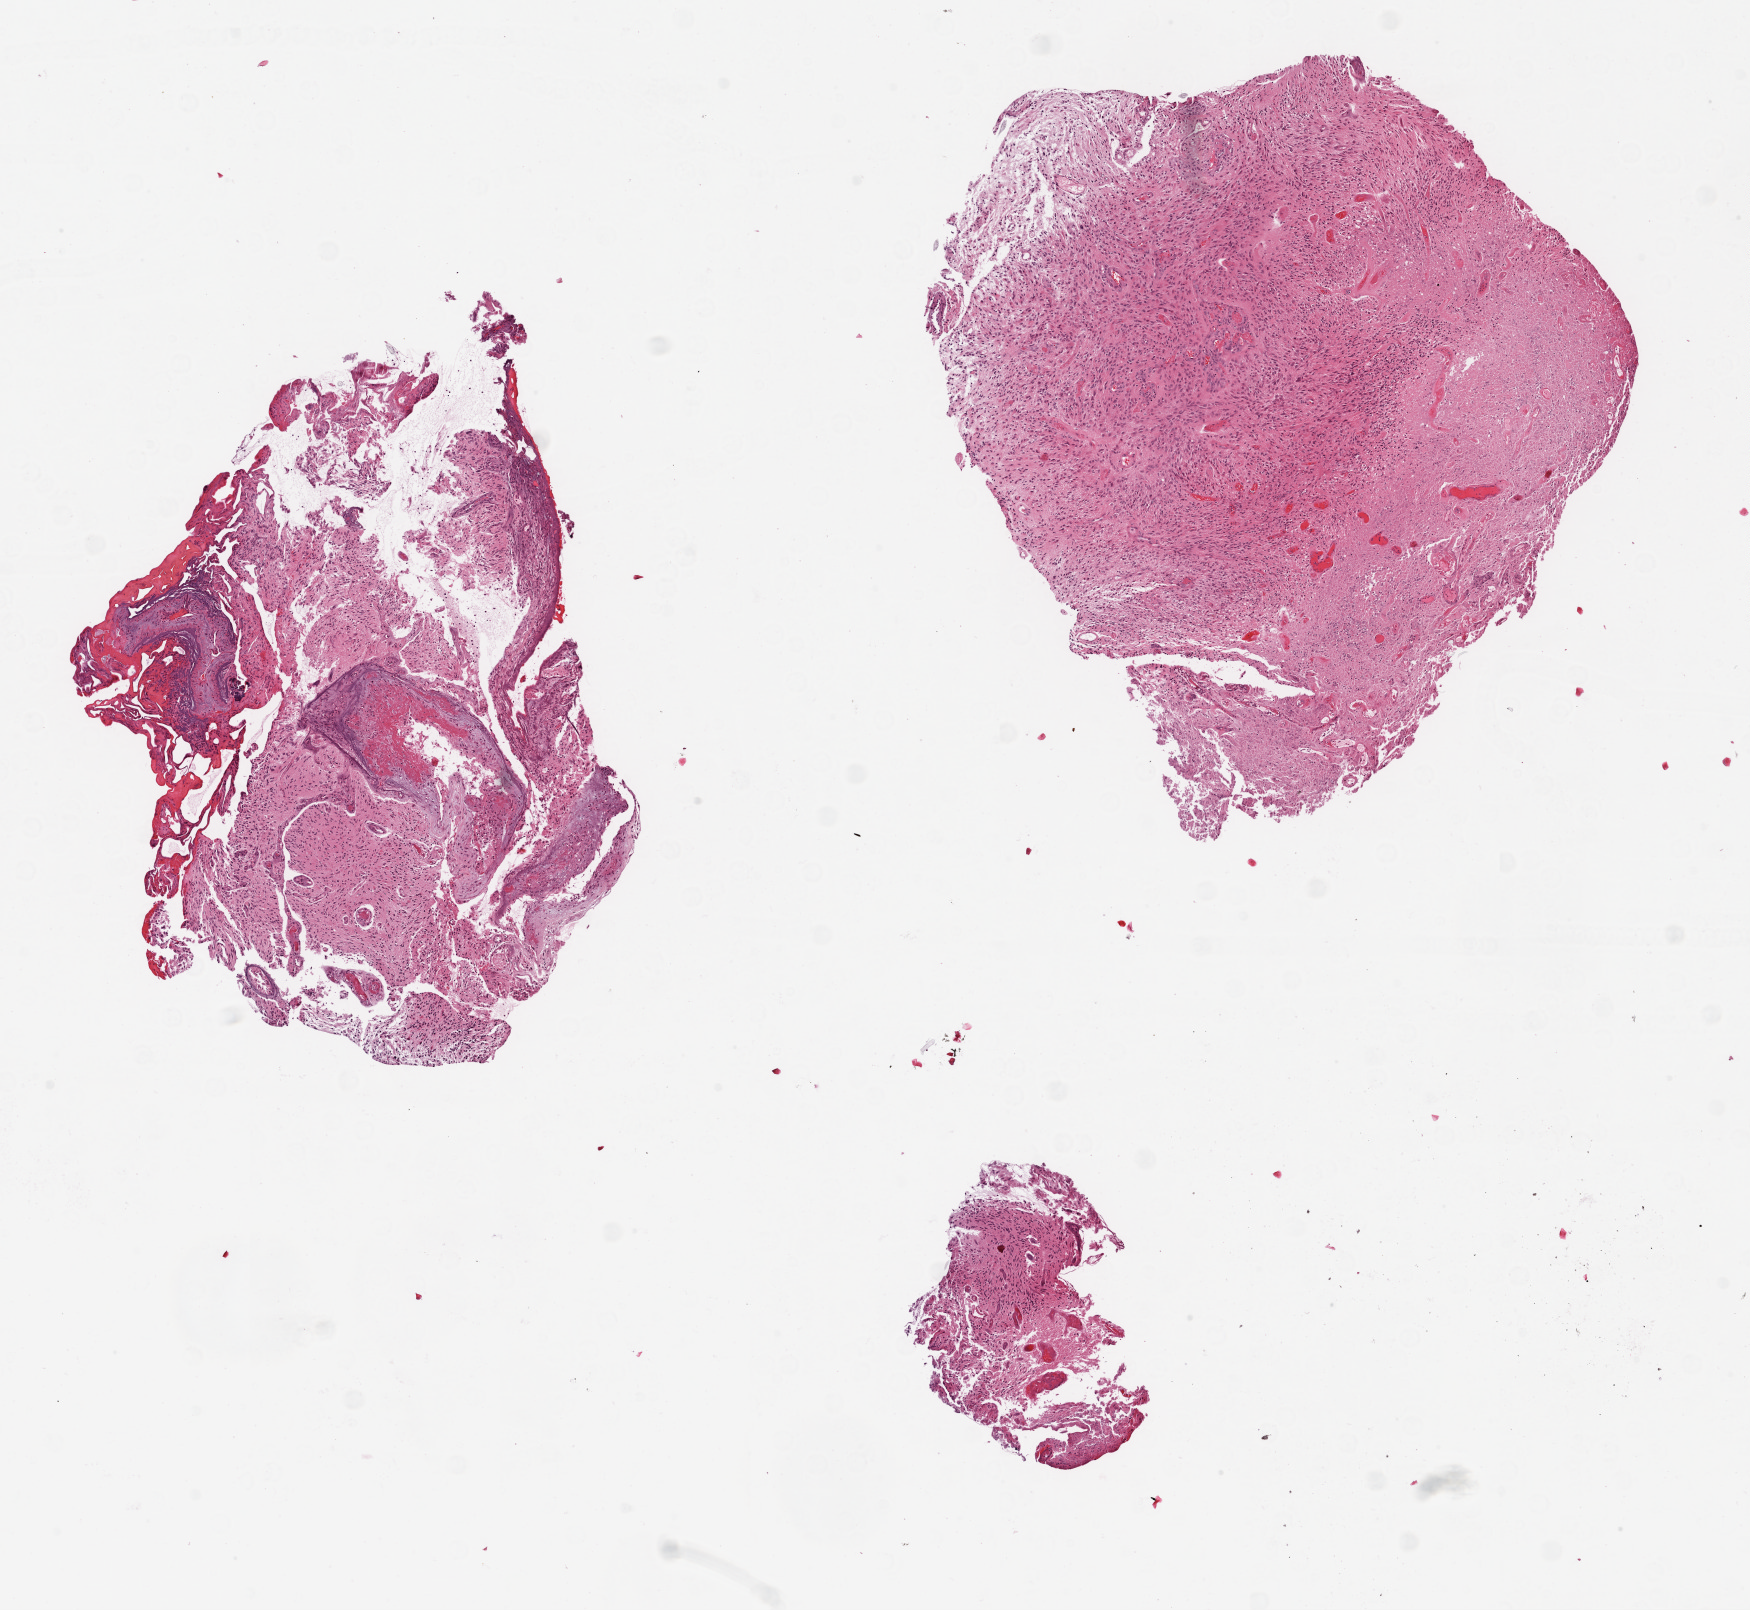
Whole-slide histology image, H&E-stained, low-resolution overview of the scanned area, about 7.0 x 6.5 mm; formalin-fixed paraffin-embedded (FFPE) diagnostic section; primary tumour sample from the brain. Patient: female, age at initial diagnosis 58 years.
Diagnosis: Glioblastoma.